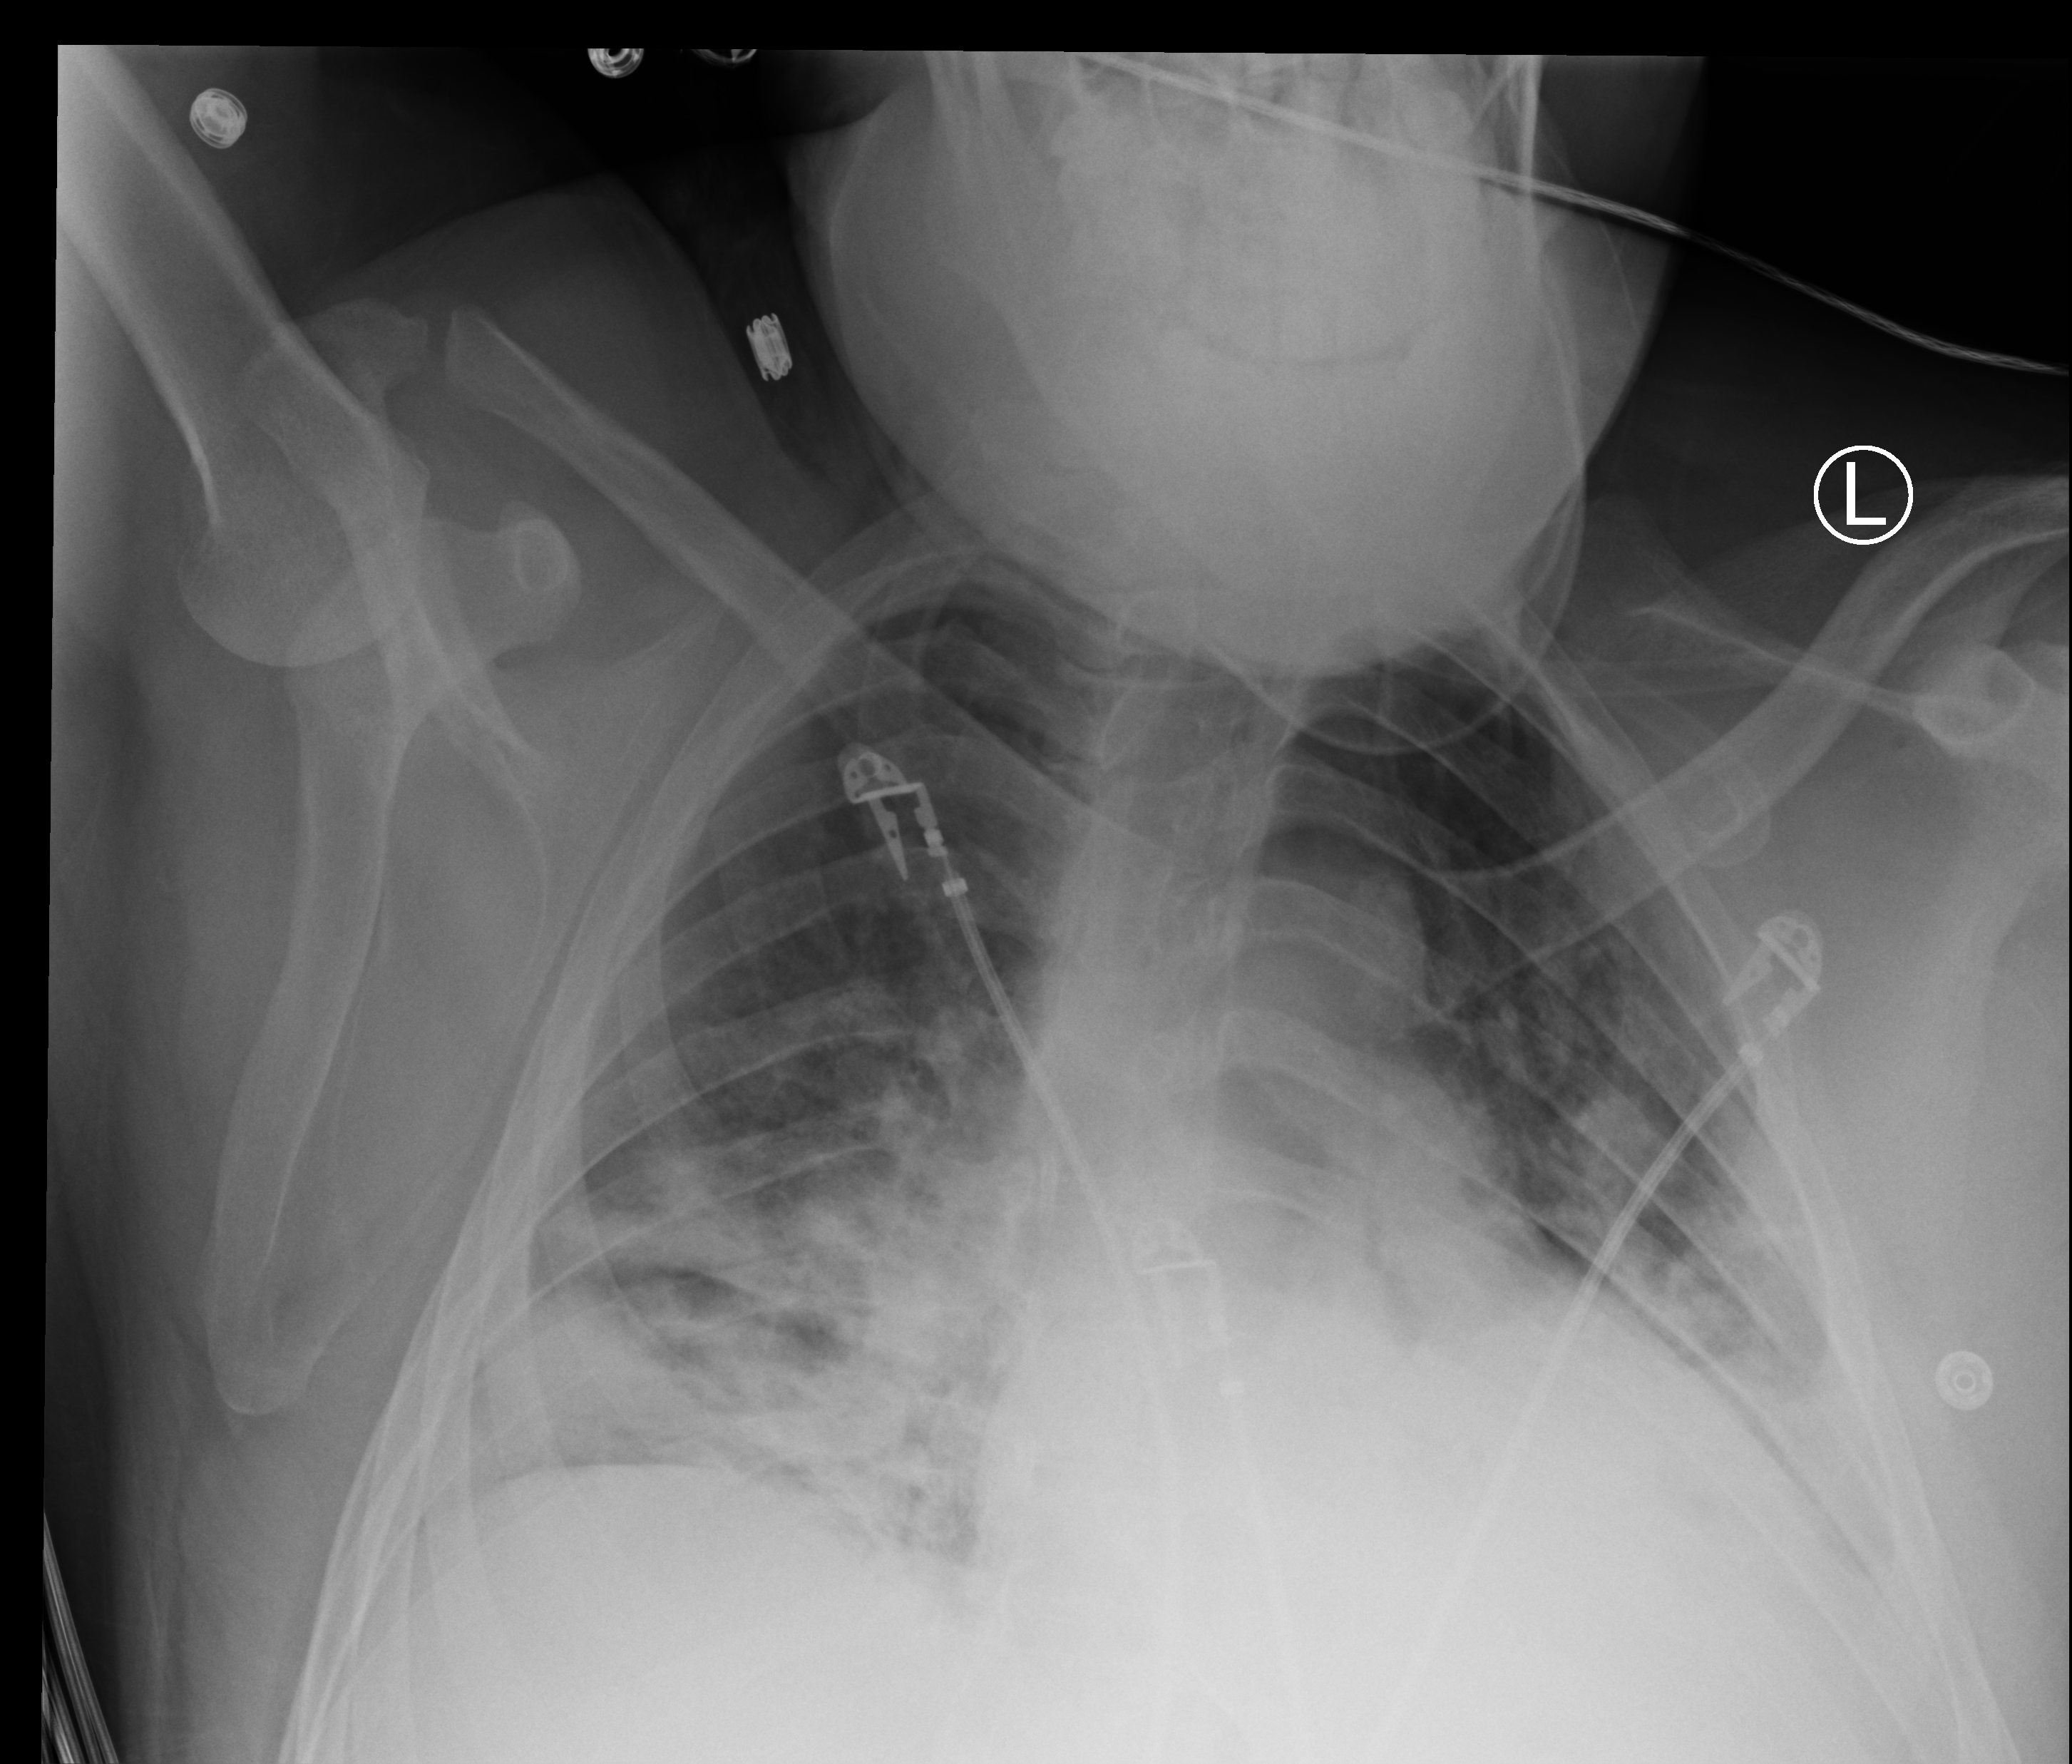
Chest X-ray (portable); anteroposterior (AP) projection. Male patient hospitalised with COVID-19, age 18–59 years.
Admission-level facts for this patient (not findings on this image; timing relative to this image not recorded): mechanically ventilated during this hospital stay: no; admitted to intensive care during this hospital stay: no.